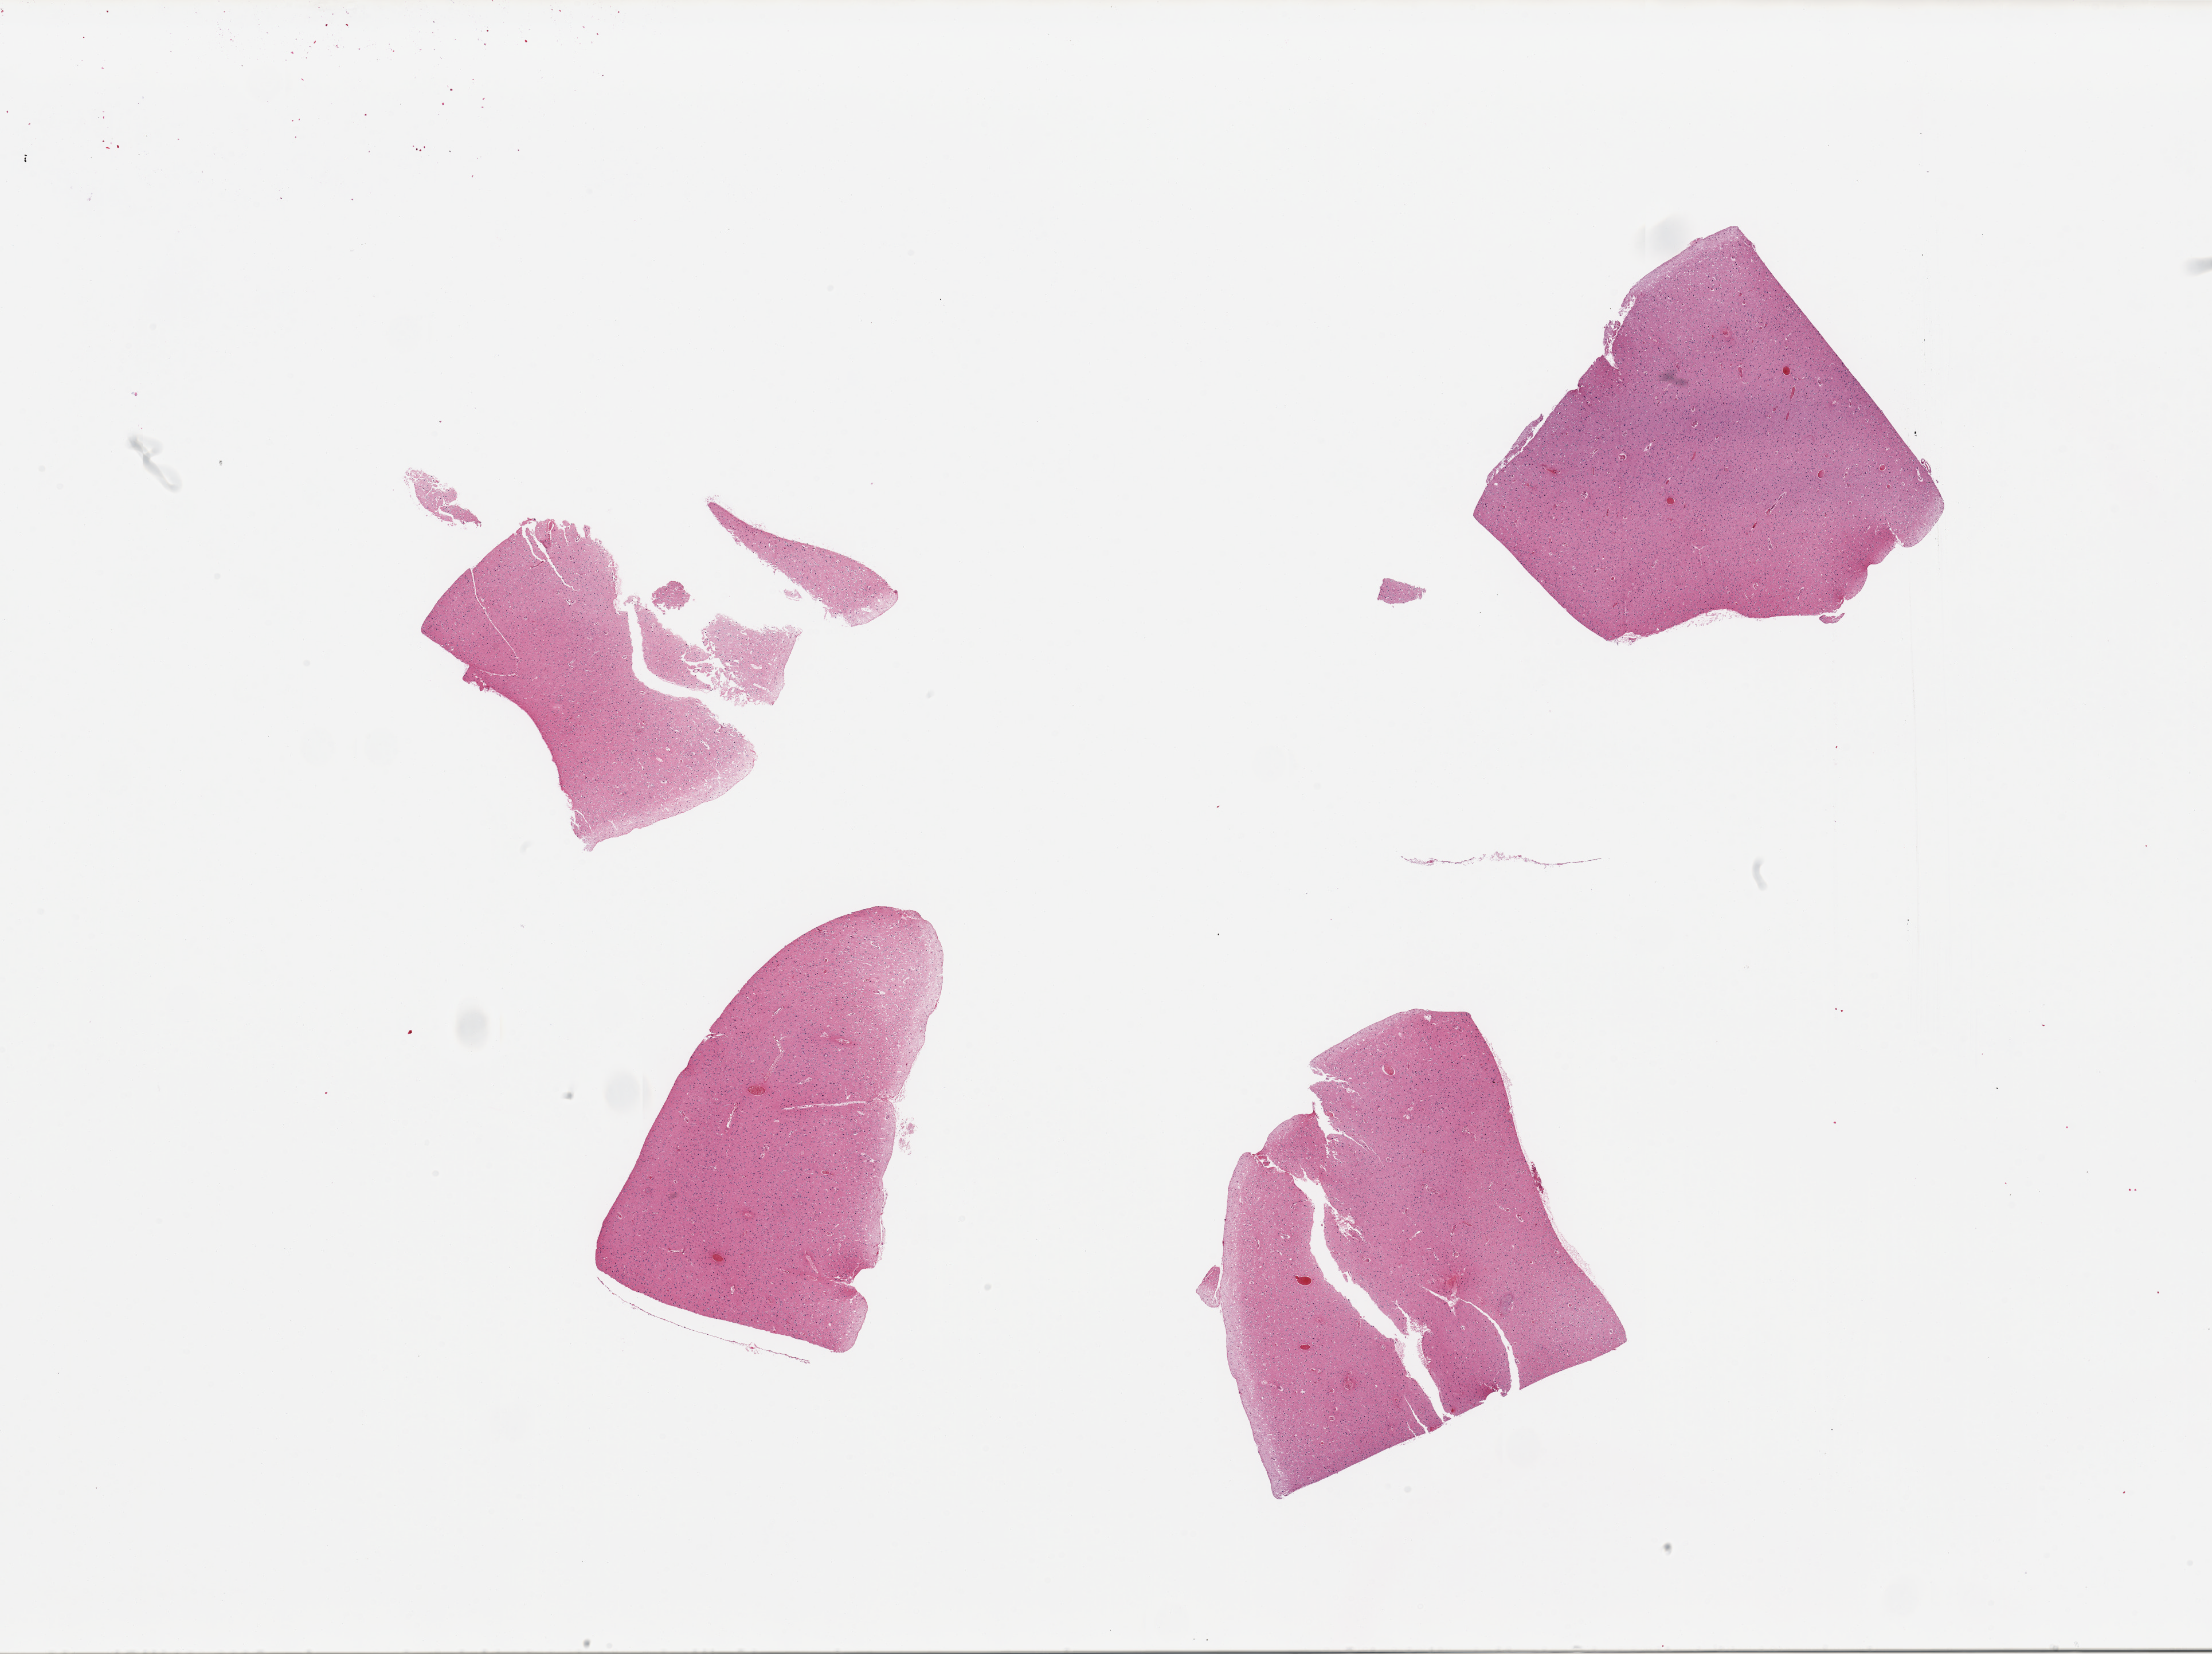
Whole-slide image, hematoxylin and eosin (H&E) stain, shown as a low-resolution overview of the whole scanned area (about 30.5 x 22.8 mm, slide scanned at 20x), PAXgene-fixed, paraffin-embedded tissue, sampled site (target tissue): cerebral cortex, tissue donor sample. Male donor.
Reviewer comment on this tissue sample: 2 pieces, no abnormalities.